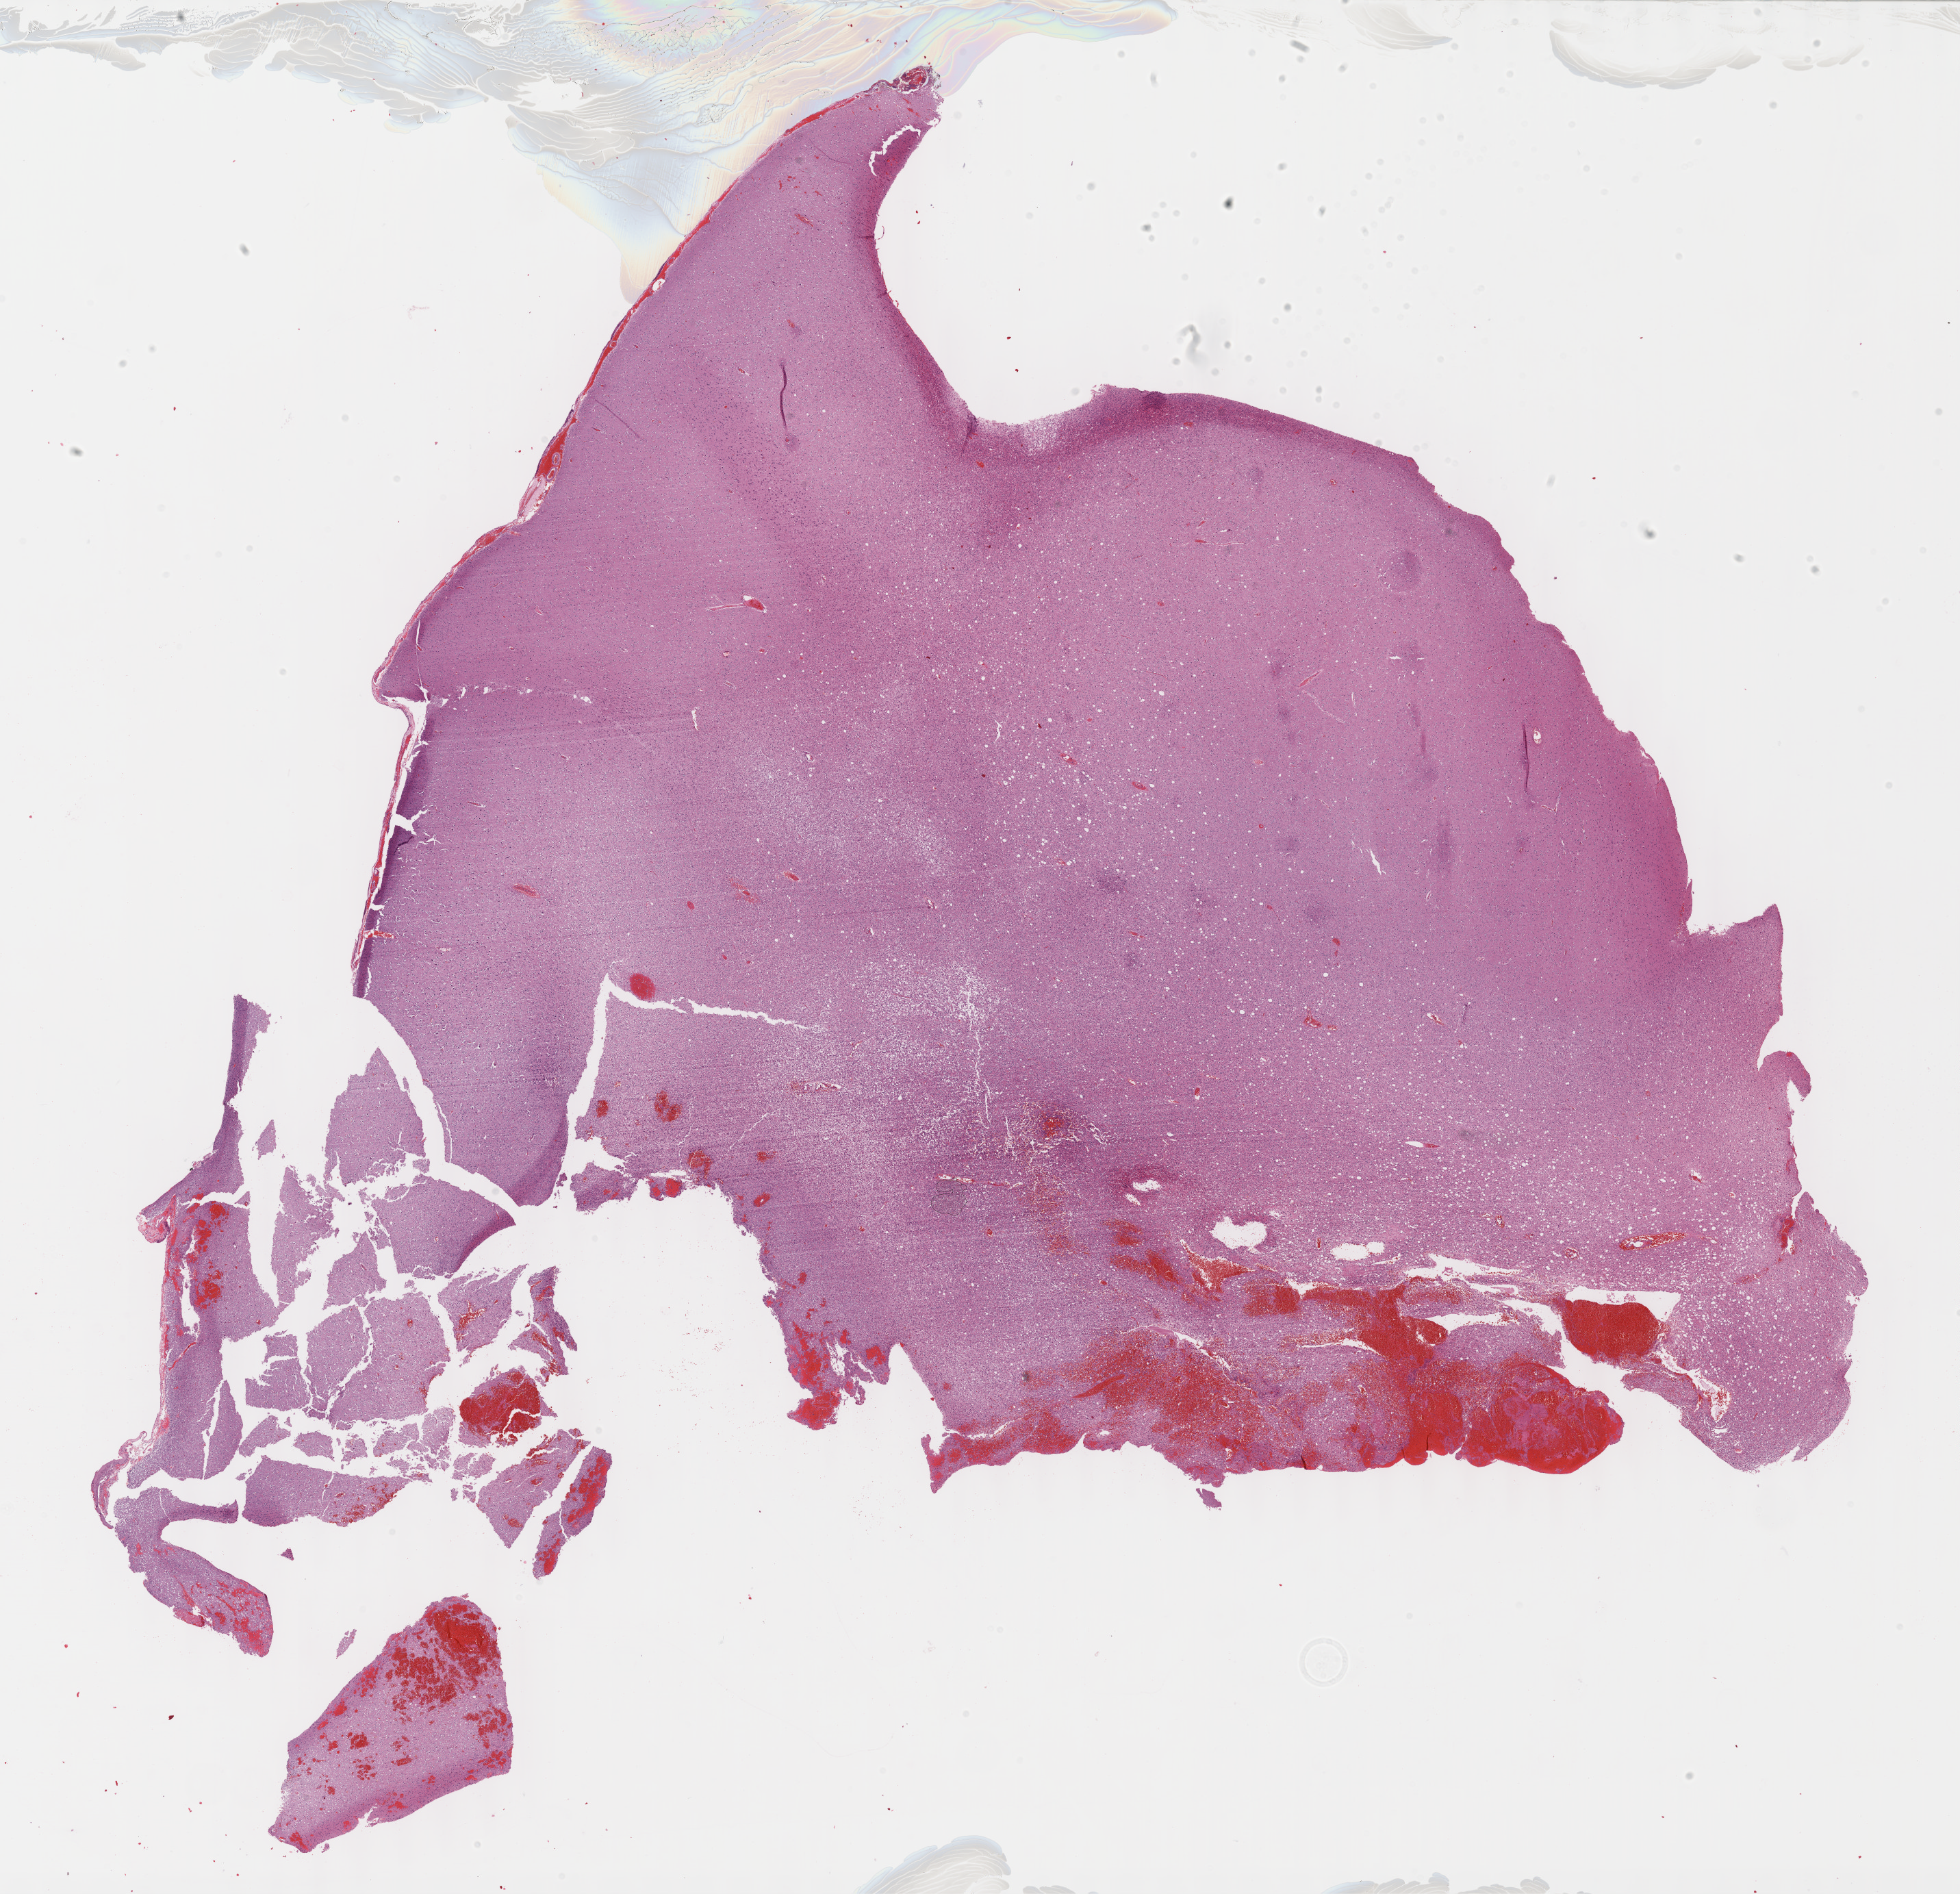
Digitized Hematoxylin and eosin (H&E) stained tissue section (whole slide), low-resolution overview of the scanned area, about 23.1 x 22.4 mm. Formalin-fixed paraffin-embedded (FFPE) diagnostic section. Primary tumour sample from the brain. Female patient; age at initial diagnosis 49 years.
Histologic diagnosis: Oligodendroglioma, NOS (cerebrum).